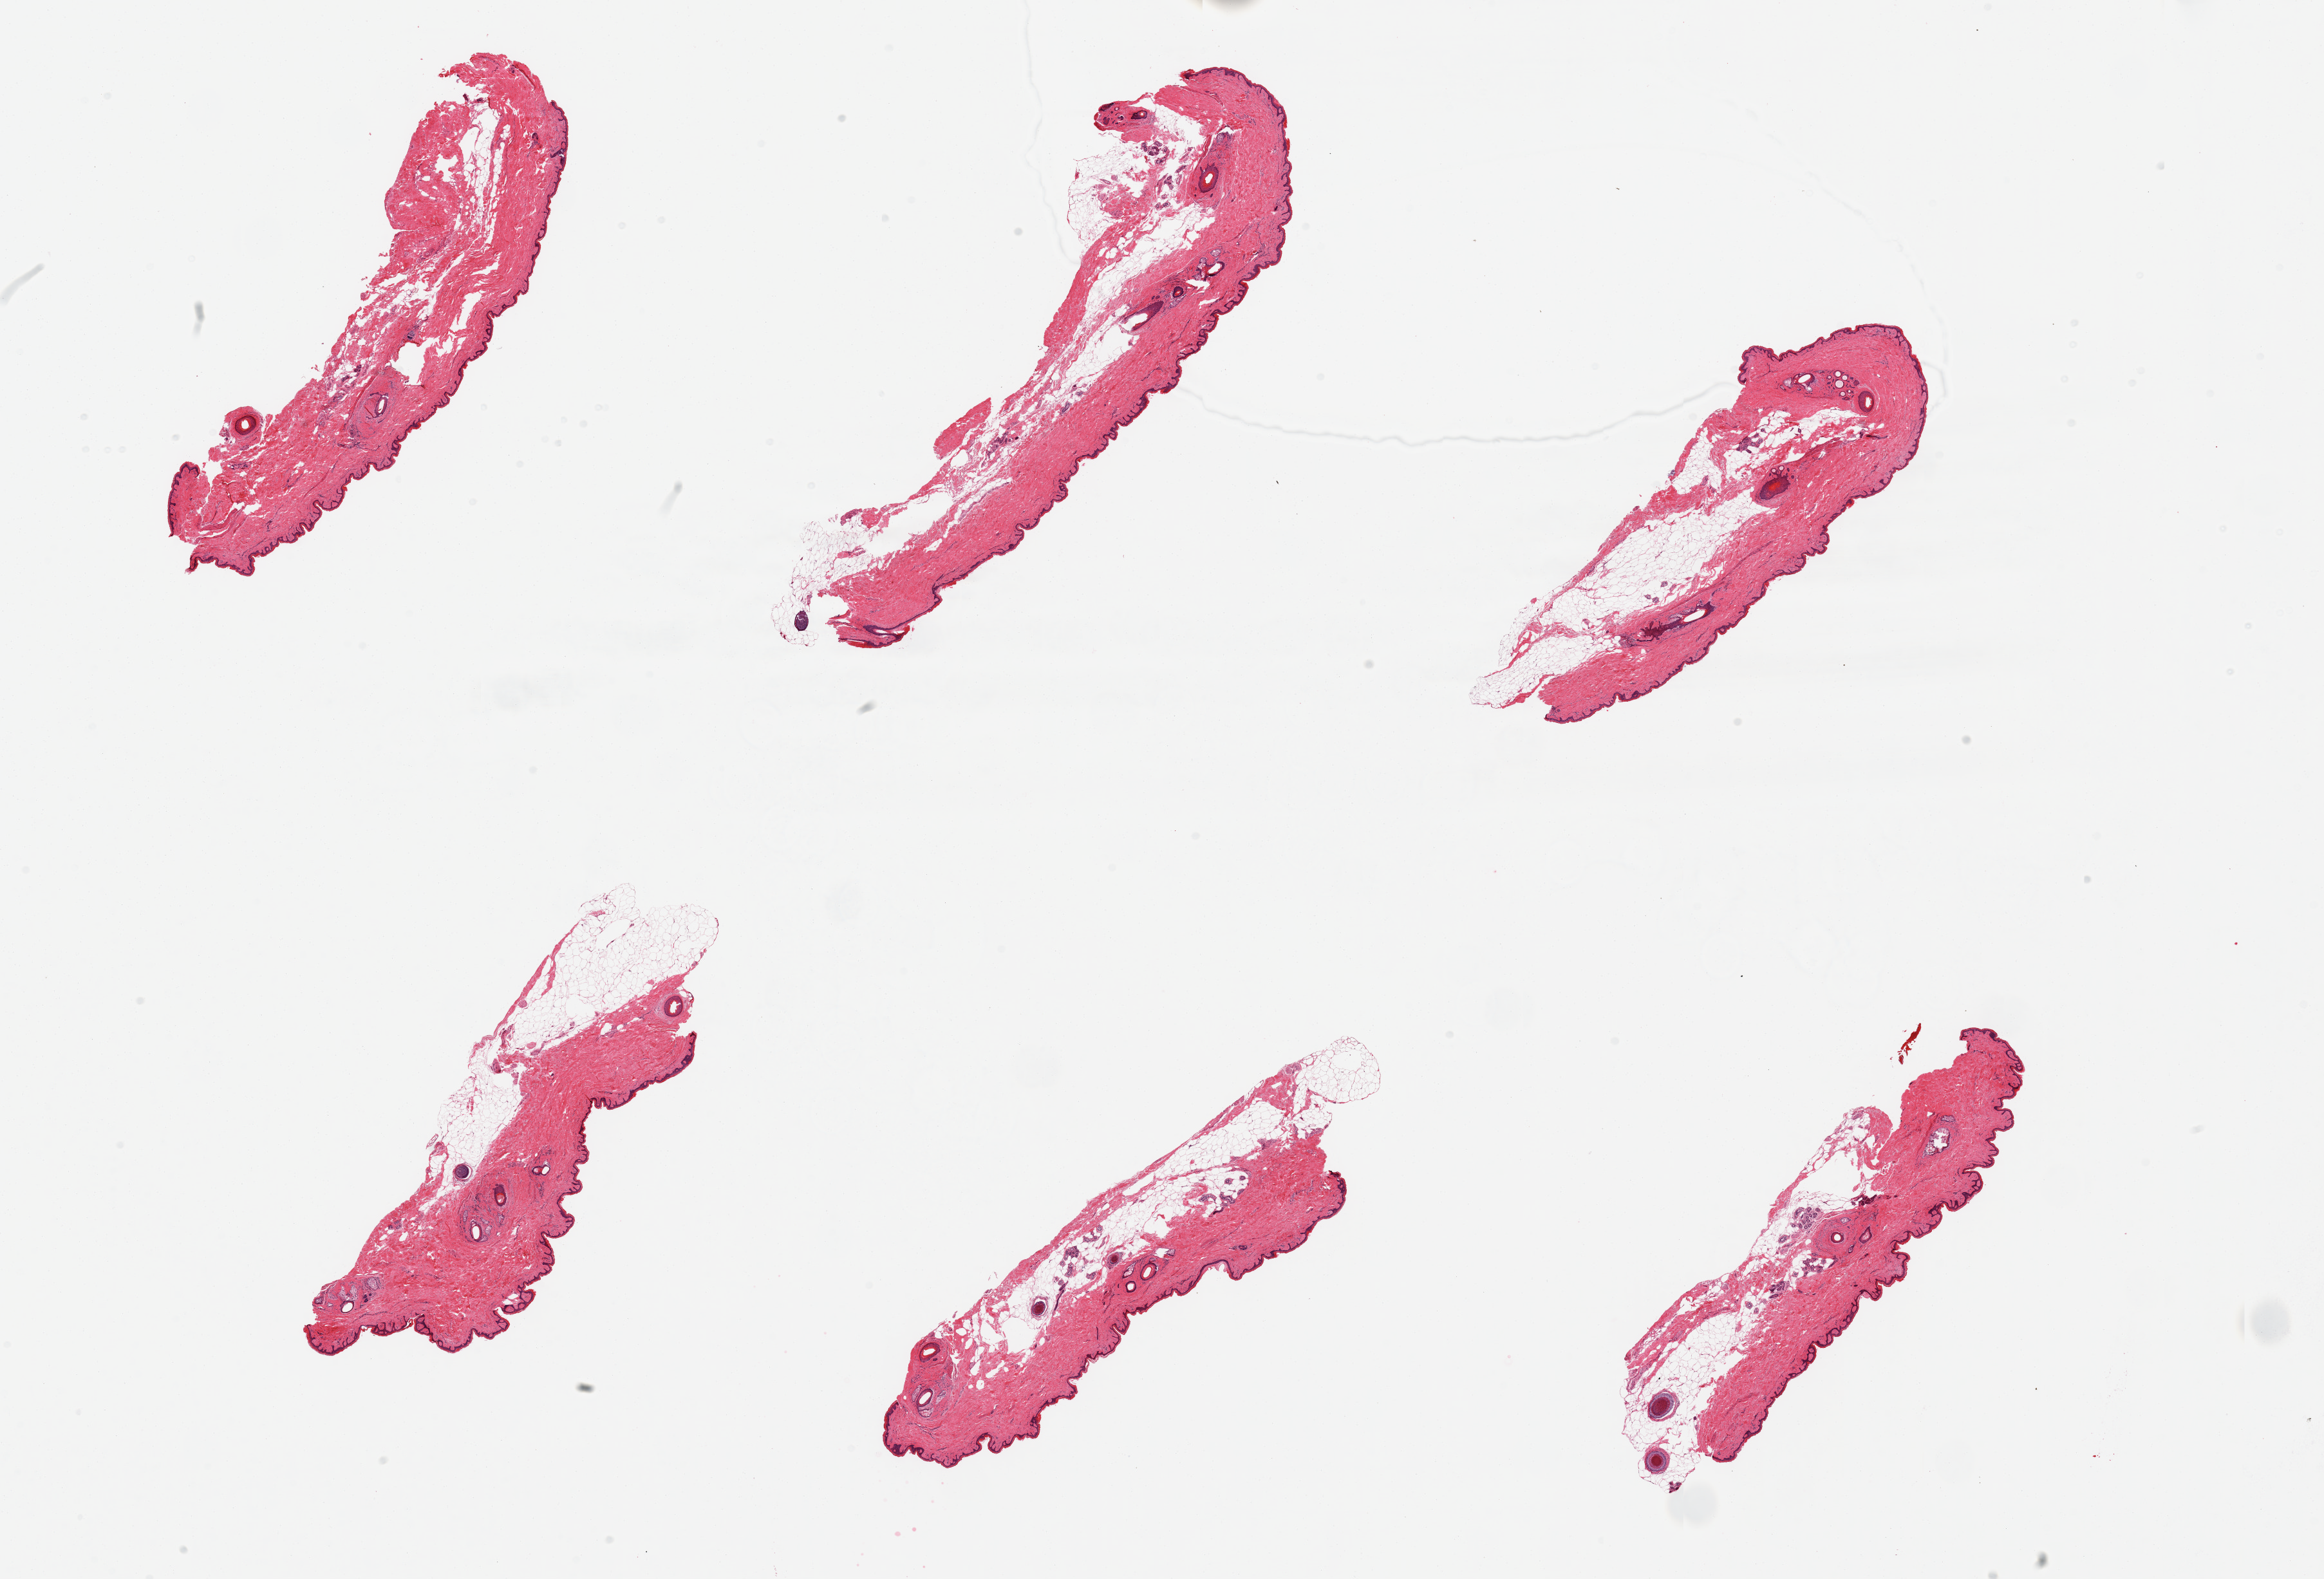
Digitized H&E-stained section, a low-resolution overview of the entire scanned area, about 28.5 x 19.4 mm (from a 20x scan). PAXgene-fixed, paraffin-embedded tissue. Sampled site (target tissue): skin of suprapubic region. Donor tissue sample. Donor: male.
Reviewer comment on this tissue sample: 6 pieces; up to 40% attached and internal fat.